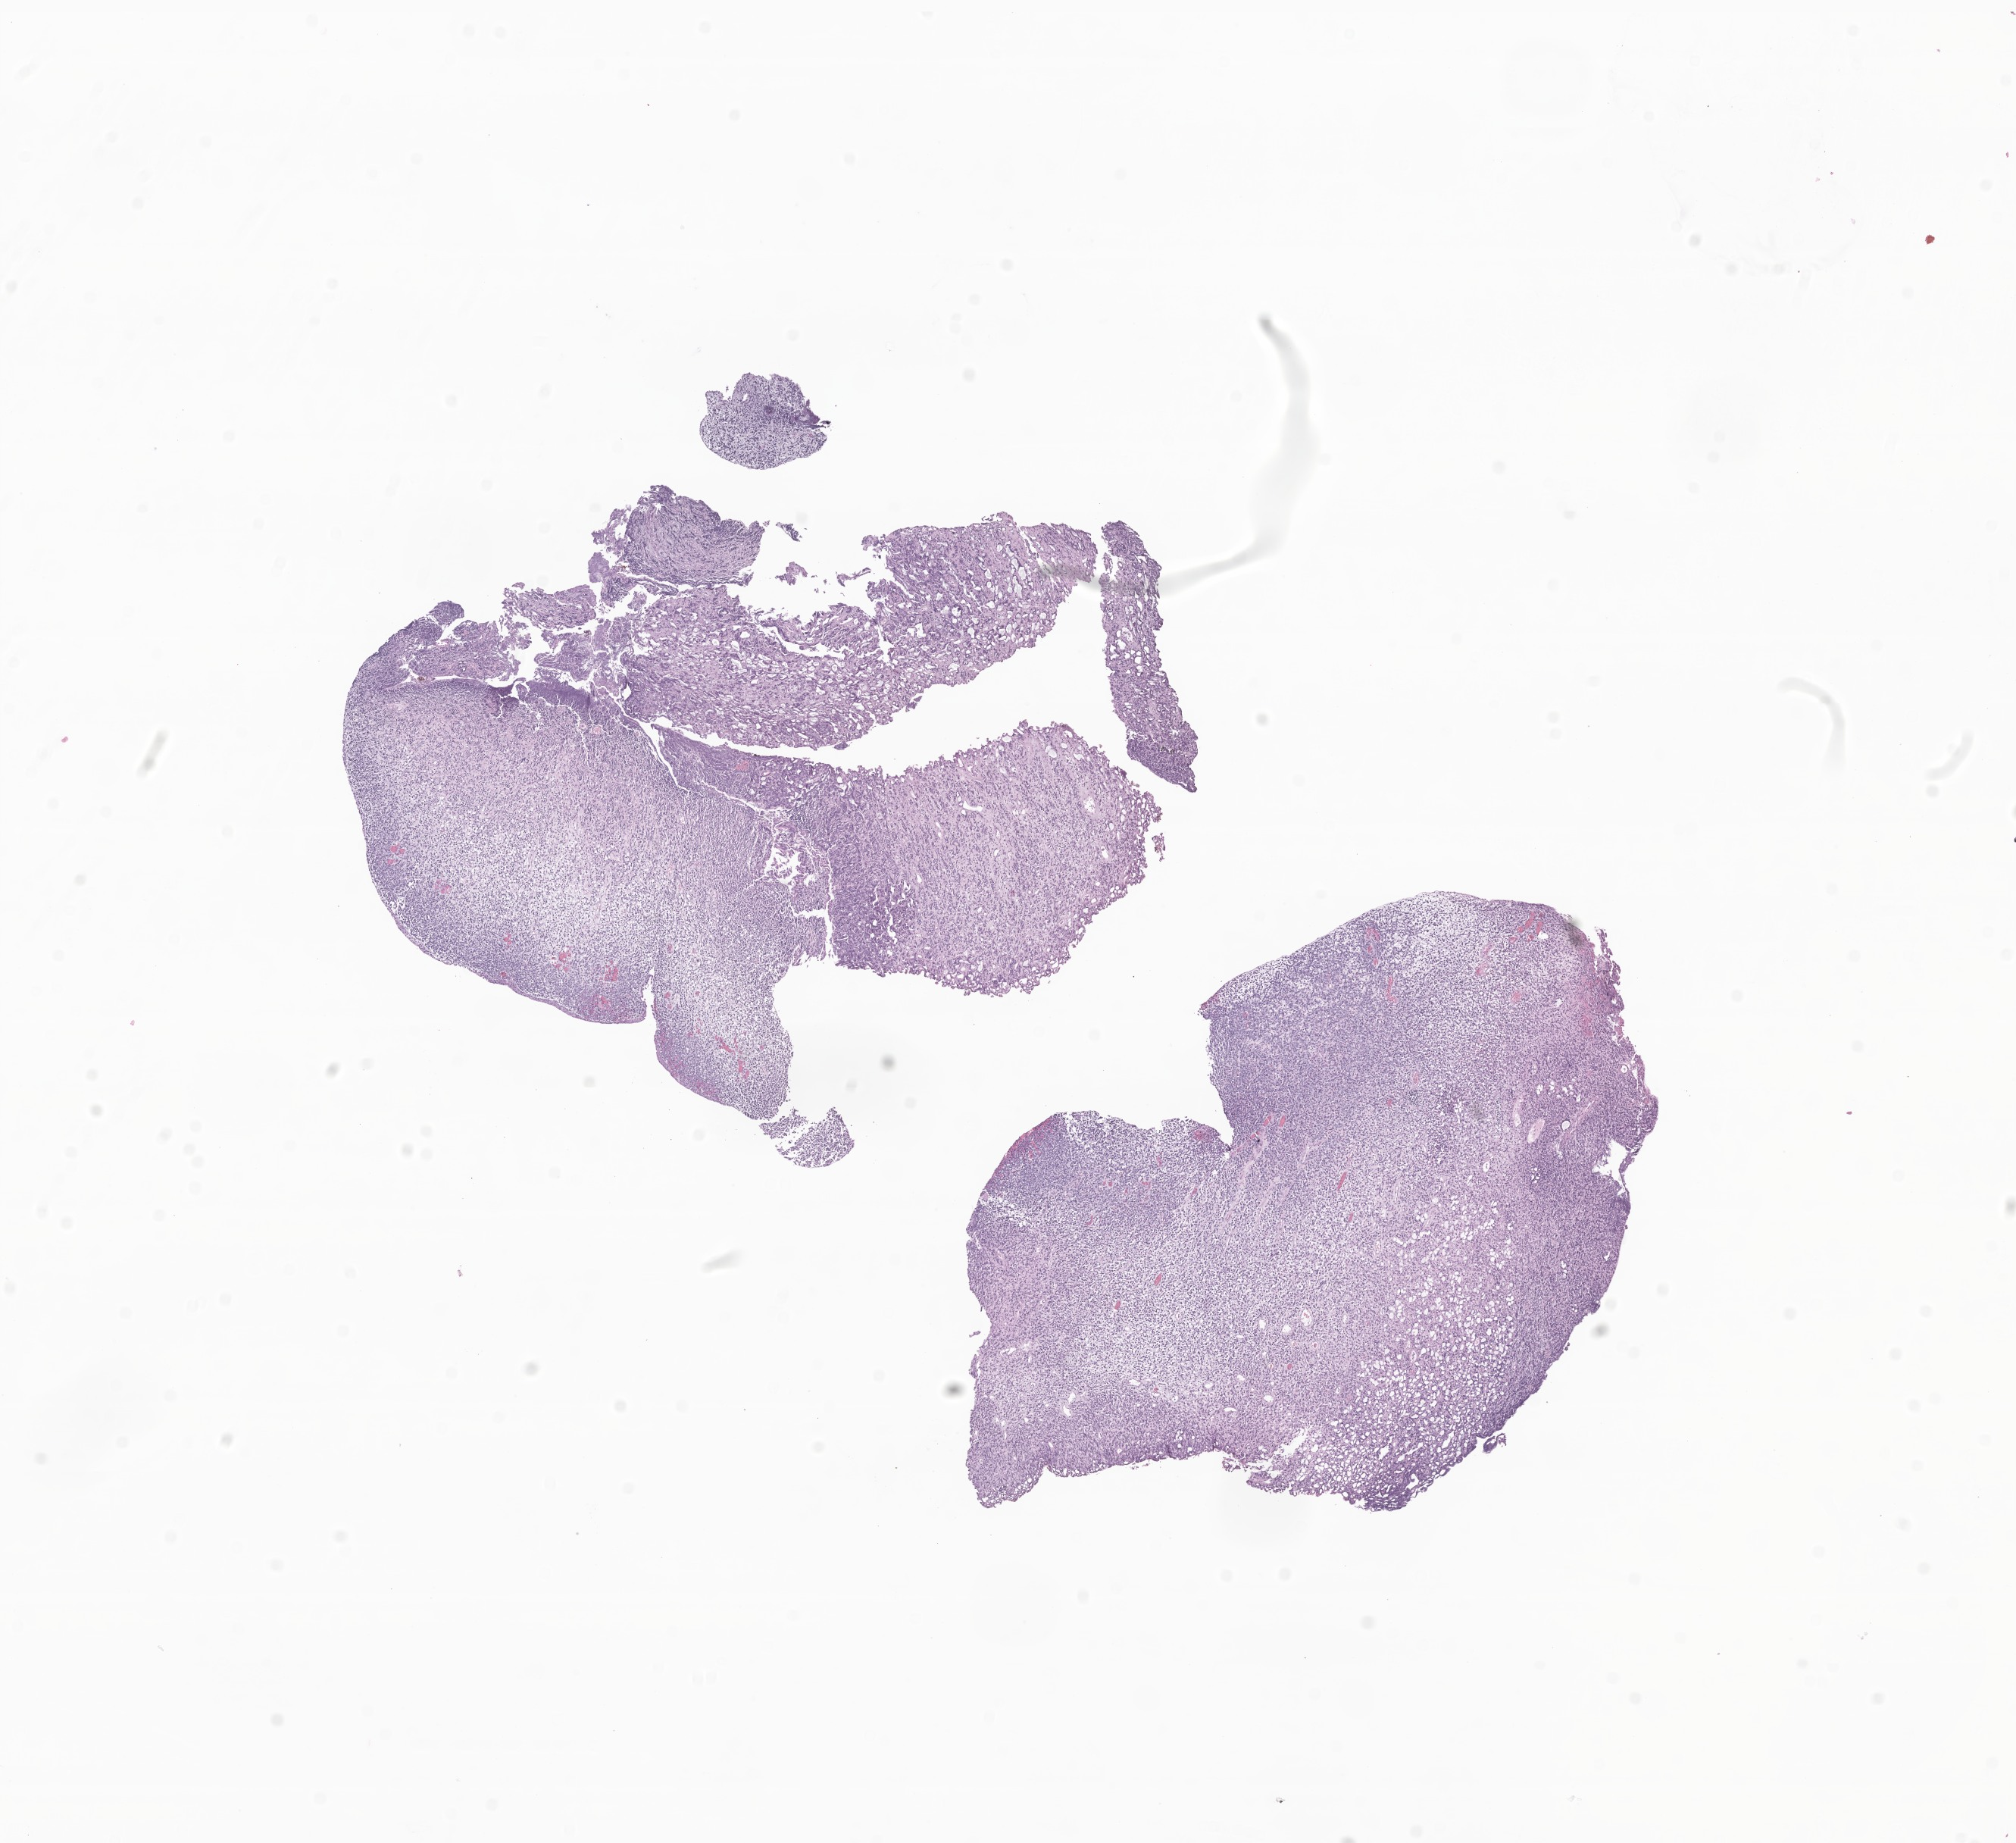
Digitized haematoxylin and eosin-stained section of tumor tissue from the prostate — low-resolution overview of the scanned area, about 11.2 x 10.3 mm, formalin-fixed, paraffin-embedded (FFPE) tissue. Patient male; age 211 months (17 years 7 months).
Diagnosis (ICD-O-3 morphology term): Rhabdomyosarcoma, NOS.